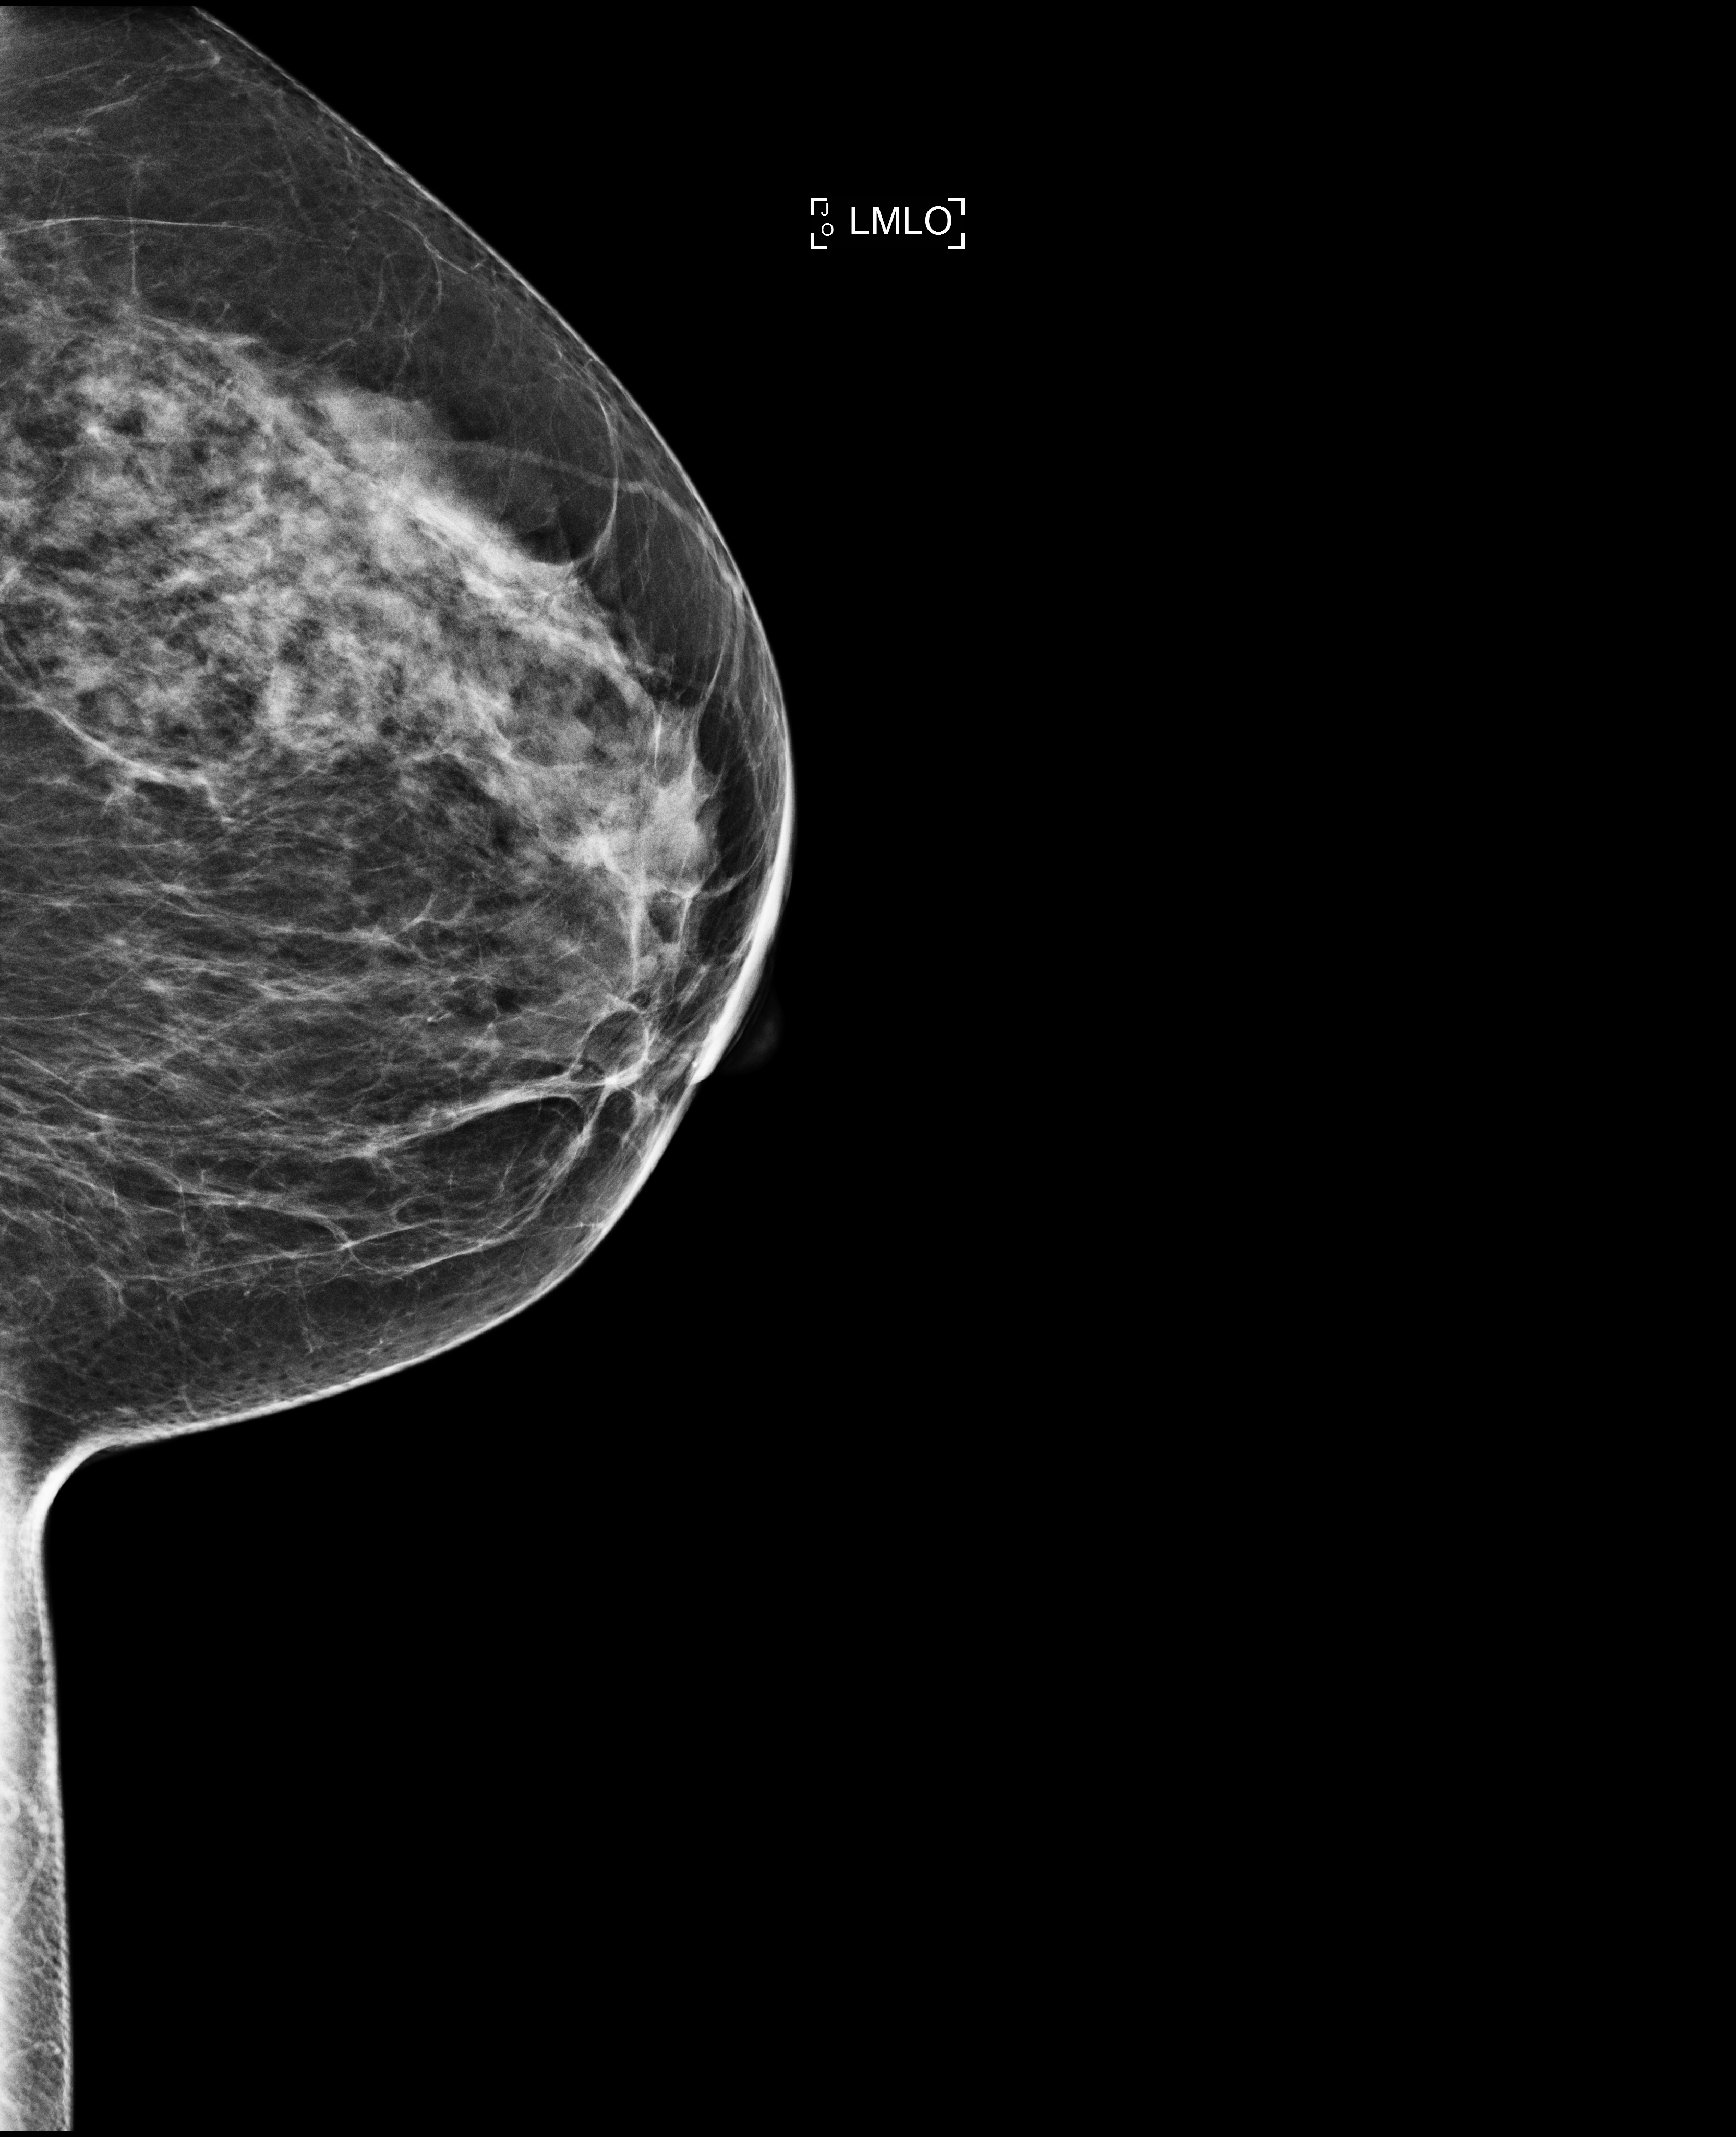
Digital mammogram (FFDM); left breast; mediolateral oblique (MLO) view; annual screening mammography examination; compressed breast thickness 56 mm. Female patient, age 57 years.
BI-RADS breast density category at the screening exam (both breasts, scale 1–4): 3. Final BI-RADS assessment for this screening round (tomosynthesis exam, both breasts): category 1. Recall: no recall after this screen.